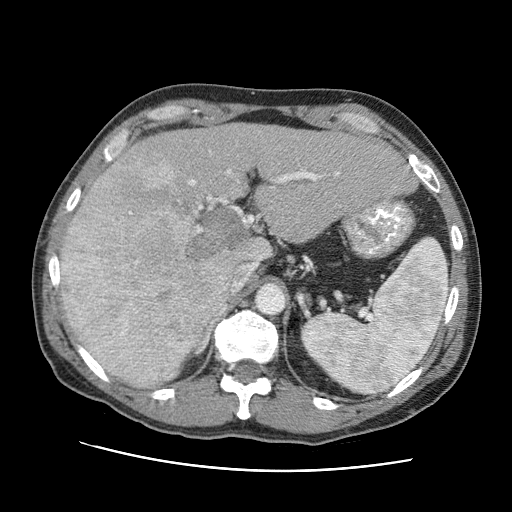
Contrast-enhanced abdominal CT (liver protocol), one axial slice; position 57 of 95 along the scan axis; 120 kVp; one of 2 acquisitions stored at this slice position; soft-tissue window (W 400 / L 40 HU); 512 × 512 image matrix, field of view 360 × 360 mm. From the clinical record (not read from this slice): diagnosis: hepatocellular carcinoma (patient treated with transarterial chemoembolisation; whether this scan precedes or follows treatment is not stated here); TNM stage (as recorded): Stage-IVA; Child-Pugh class: A; tumour differentiation: moderately differentiated; tumour nodularity: multinodular.
Outlined on this slice (semi-automatically segmented with operator editing):
- liver parenchyma outside the tumour (the mass and vessels are separate outlines, so this box may not span the whole liver): bounding box (x1, y1, x2, y2) in pixels: (60, 122, 416, 386)
- mass: (61, 157, 247, 386)
- liver vessels: (168, 151, 339, 378)